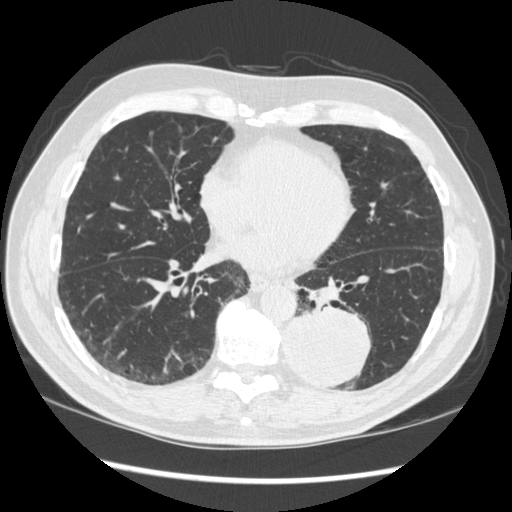
Low-dose screening chest CT, axial slice; first (baseline) screen; lung window (W 1500 / L -600 HU); 1.25 mm slice thickness; 120 kVp; 512 × 512 image matrix. Male participant, aged 72 years at enrolment. Current smoker at enrolment.
- Expert reader's lesion annotation, bounding box (x1, y1, x2, y2) in pixels: (271, 299, 375, 389).
- The screening reader recorded 2 non-calcified nodules or masses ≥4 mm on this exam (left lower lobe, right middle lobe); which of them this box marks is not recorded.
- Lung cancer was diagnosed 37 days after this screen: squamous cell carcinoma, NOS, left lower lobe, stage IIIA (AJCC 6th edition), 60 mm at pathology.